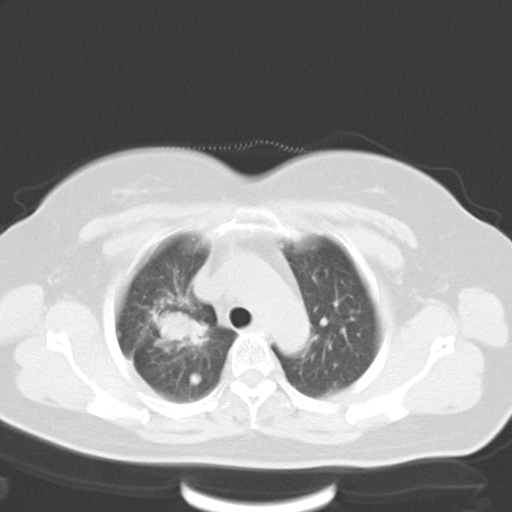
Chest CT, one axial slice. Slice 24 of 30 in the series (ordered by position). Reconstruction kernel B40f. 120 kVp. Lung window (W 1500 / L -600 HU). 8 mm slice thickness. 512 × 512 image matrix, field of view 353 × 353 mm. Female patient, age 50 years. Case-level facts recorded for this patient, not image findings: clinical TNM (as recorded): T2a N0 M1a.
Outlined on this slice (bounding box drawn by a radiologist):
- lung tumour (recorded histology: adenocarcinoma): bounding box <144,303,212,348> (left, top, right, bottom; pixels)